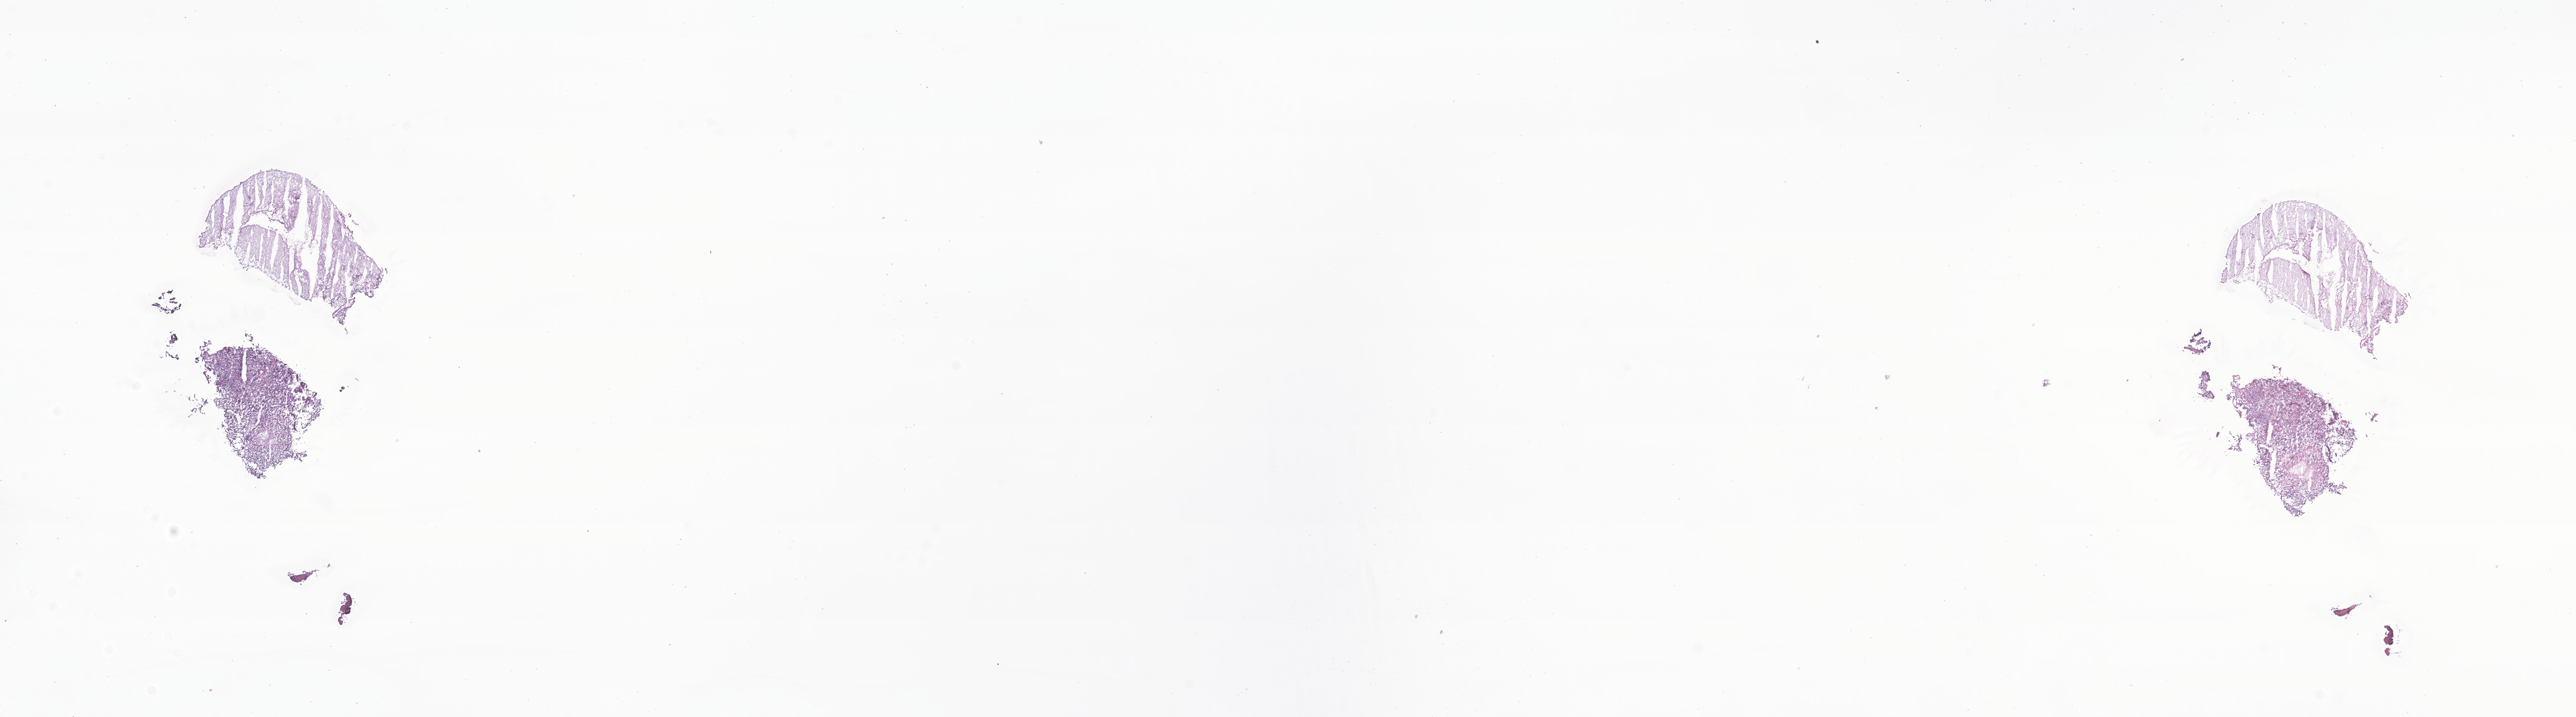
Digitized H&E-stained section of tumor tissue from the brain stem — shown as a low-resolution overview of the whole scanned area (about 28.4 x 7.9 mm); frozen section (OCT-embedded). Patient: male, age 34 months (2 years 10 months).
* diagnosis: Atypical teratoid/rhabdoid tumor